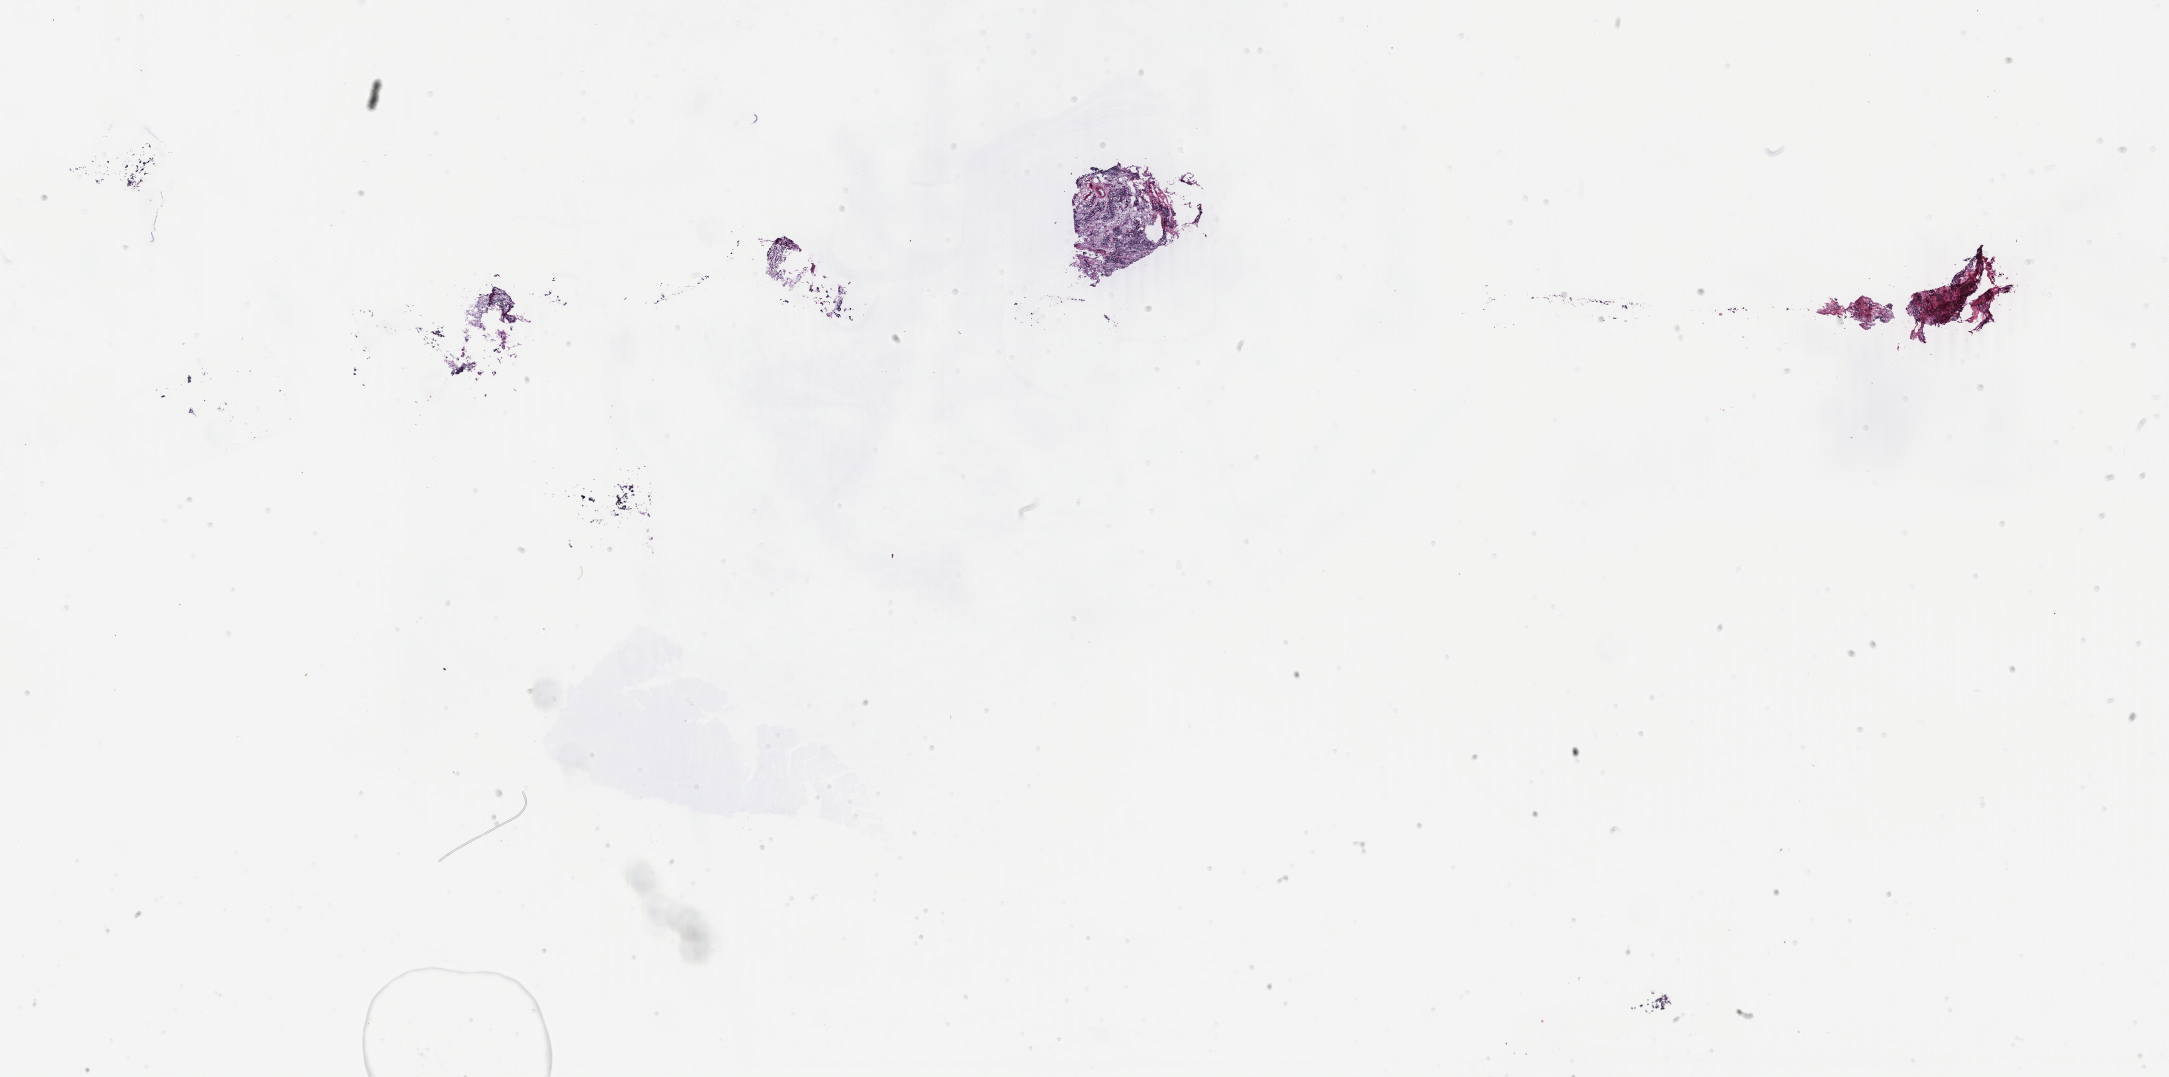
Whole-slide histology image, H&E-stained — whole scanned area (about 34.5 x 17.1 mm) shown as a low-resolution overview. Frozen section from the top of the tissue portion. Sample: primary tumour, breast. Female, age 73 years at initial diagnosis. Composition of this section per pathologist review: tumour cells 30%, tumour nuclei 75%, normal cells 5%, stromal cells 64%, necrosis 1%. Inflammatory infiltration, as recorded: lymphocyte infiltration 5%, monocyte infiltration 2%, neutrophil infiltration 0%.
• TNM: T1 N0 (i-) M0
• laterality: right
• lymph nodes positive (case pathology): 0 of 1 examined
• histologic diagnosis: Infiltrating duct carcinoma, NOS
• AJCC pathologic stage: IA (5th edition)